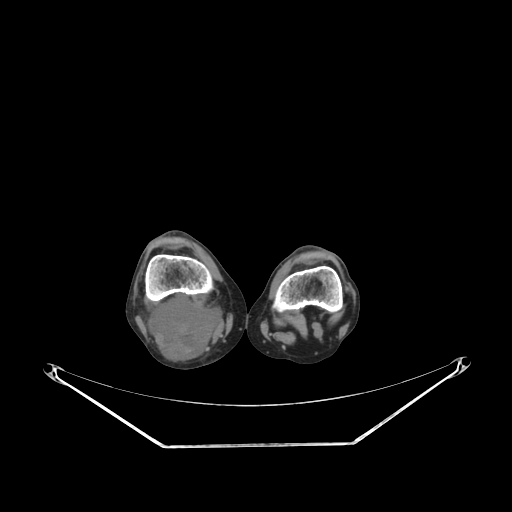
CT of an extremity soft-tissue mass (from a PET/CT study), one axial slice; slice 173 of 267 in the series (ordered by position); reconstruction kernel SOFT; 140 kVp; soft-tissue window (W 400 / L 40 HU); 3.75 mm slice thickness; 512 × 512 image matrix. Female patient. Case-level facts recorded for this patient, not image findings: histological type: liposarcoma; site of the primary tumour: right thigh.
Annotated regions visible in this slice (expert contour drawn on MRI and transferred to this co-registered scan by the dataset authors):
- gross tumour volume (mass): box from (x=146, y=292) to (x=223, y=360) px